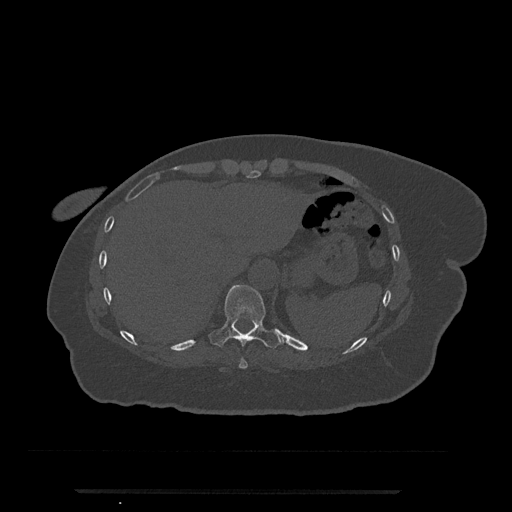
CT including the spine, one axial slice. Slice 293 of 797 in the series (ordered by position). Bone window (W 1800 / L 400 HU). 0.5 mm slice thickness. 512 × 512 image matrix, field of view 440 × 440 mm. Patient: female, 51 years. Case-level facts recorded for this patient, not image findings: primary cancer: neuro; vertebrae with lytic lesions (as recorded): T8.
Structures marked on this image (semi-automatic segmentation, software-assisted and operator-edited):
- T10 vertebra: bounding box <210,285,281,349> (left, top, right, bottom; pixels)
- T9 vertebra: <239,357,248,369>